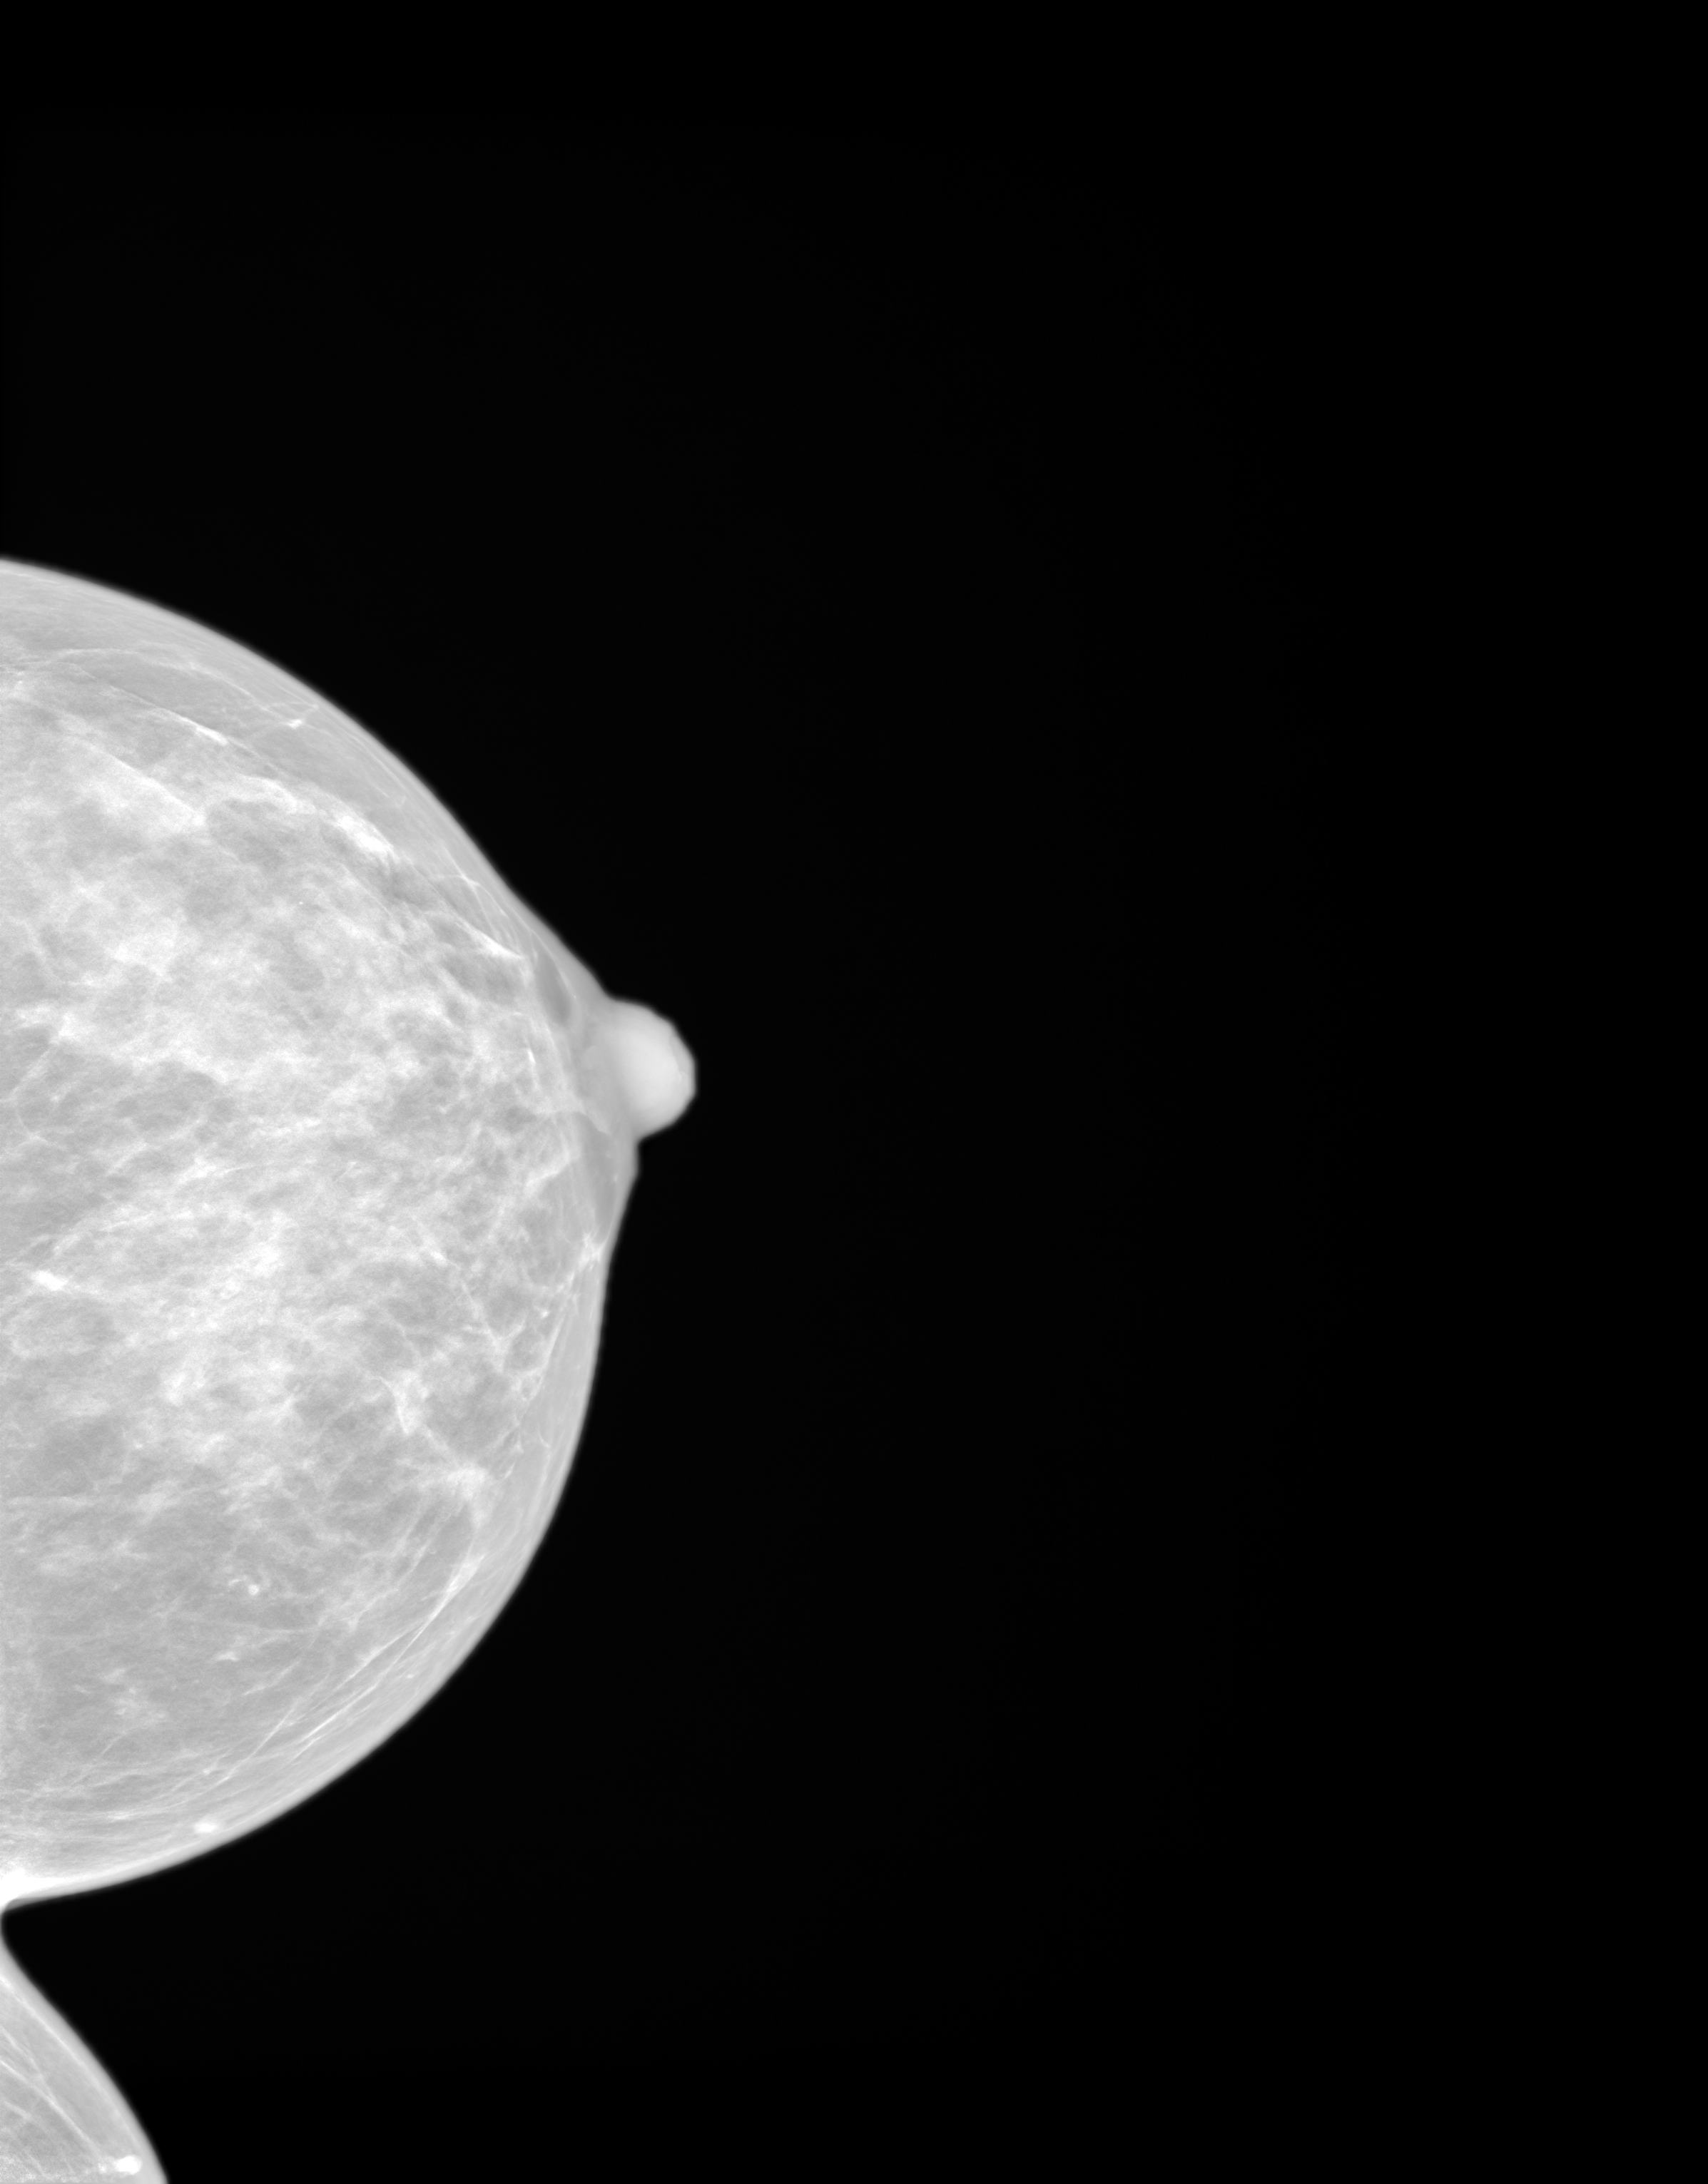
Synthesized 2-D mammogram reconstructed from digital breast tomosynthesis; left breast; CC view; screening examination. Patient aged 42 years (female).
Breast density at the screening exam (both breasts): extremely dense (BI-RADS density category d). Final BI-RADS assessment for this screening round (tomosynthesis exam, both breasts): category 1. Recall: no recall after this screen.